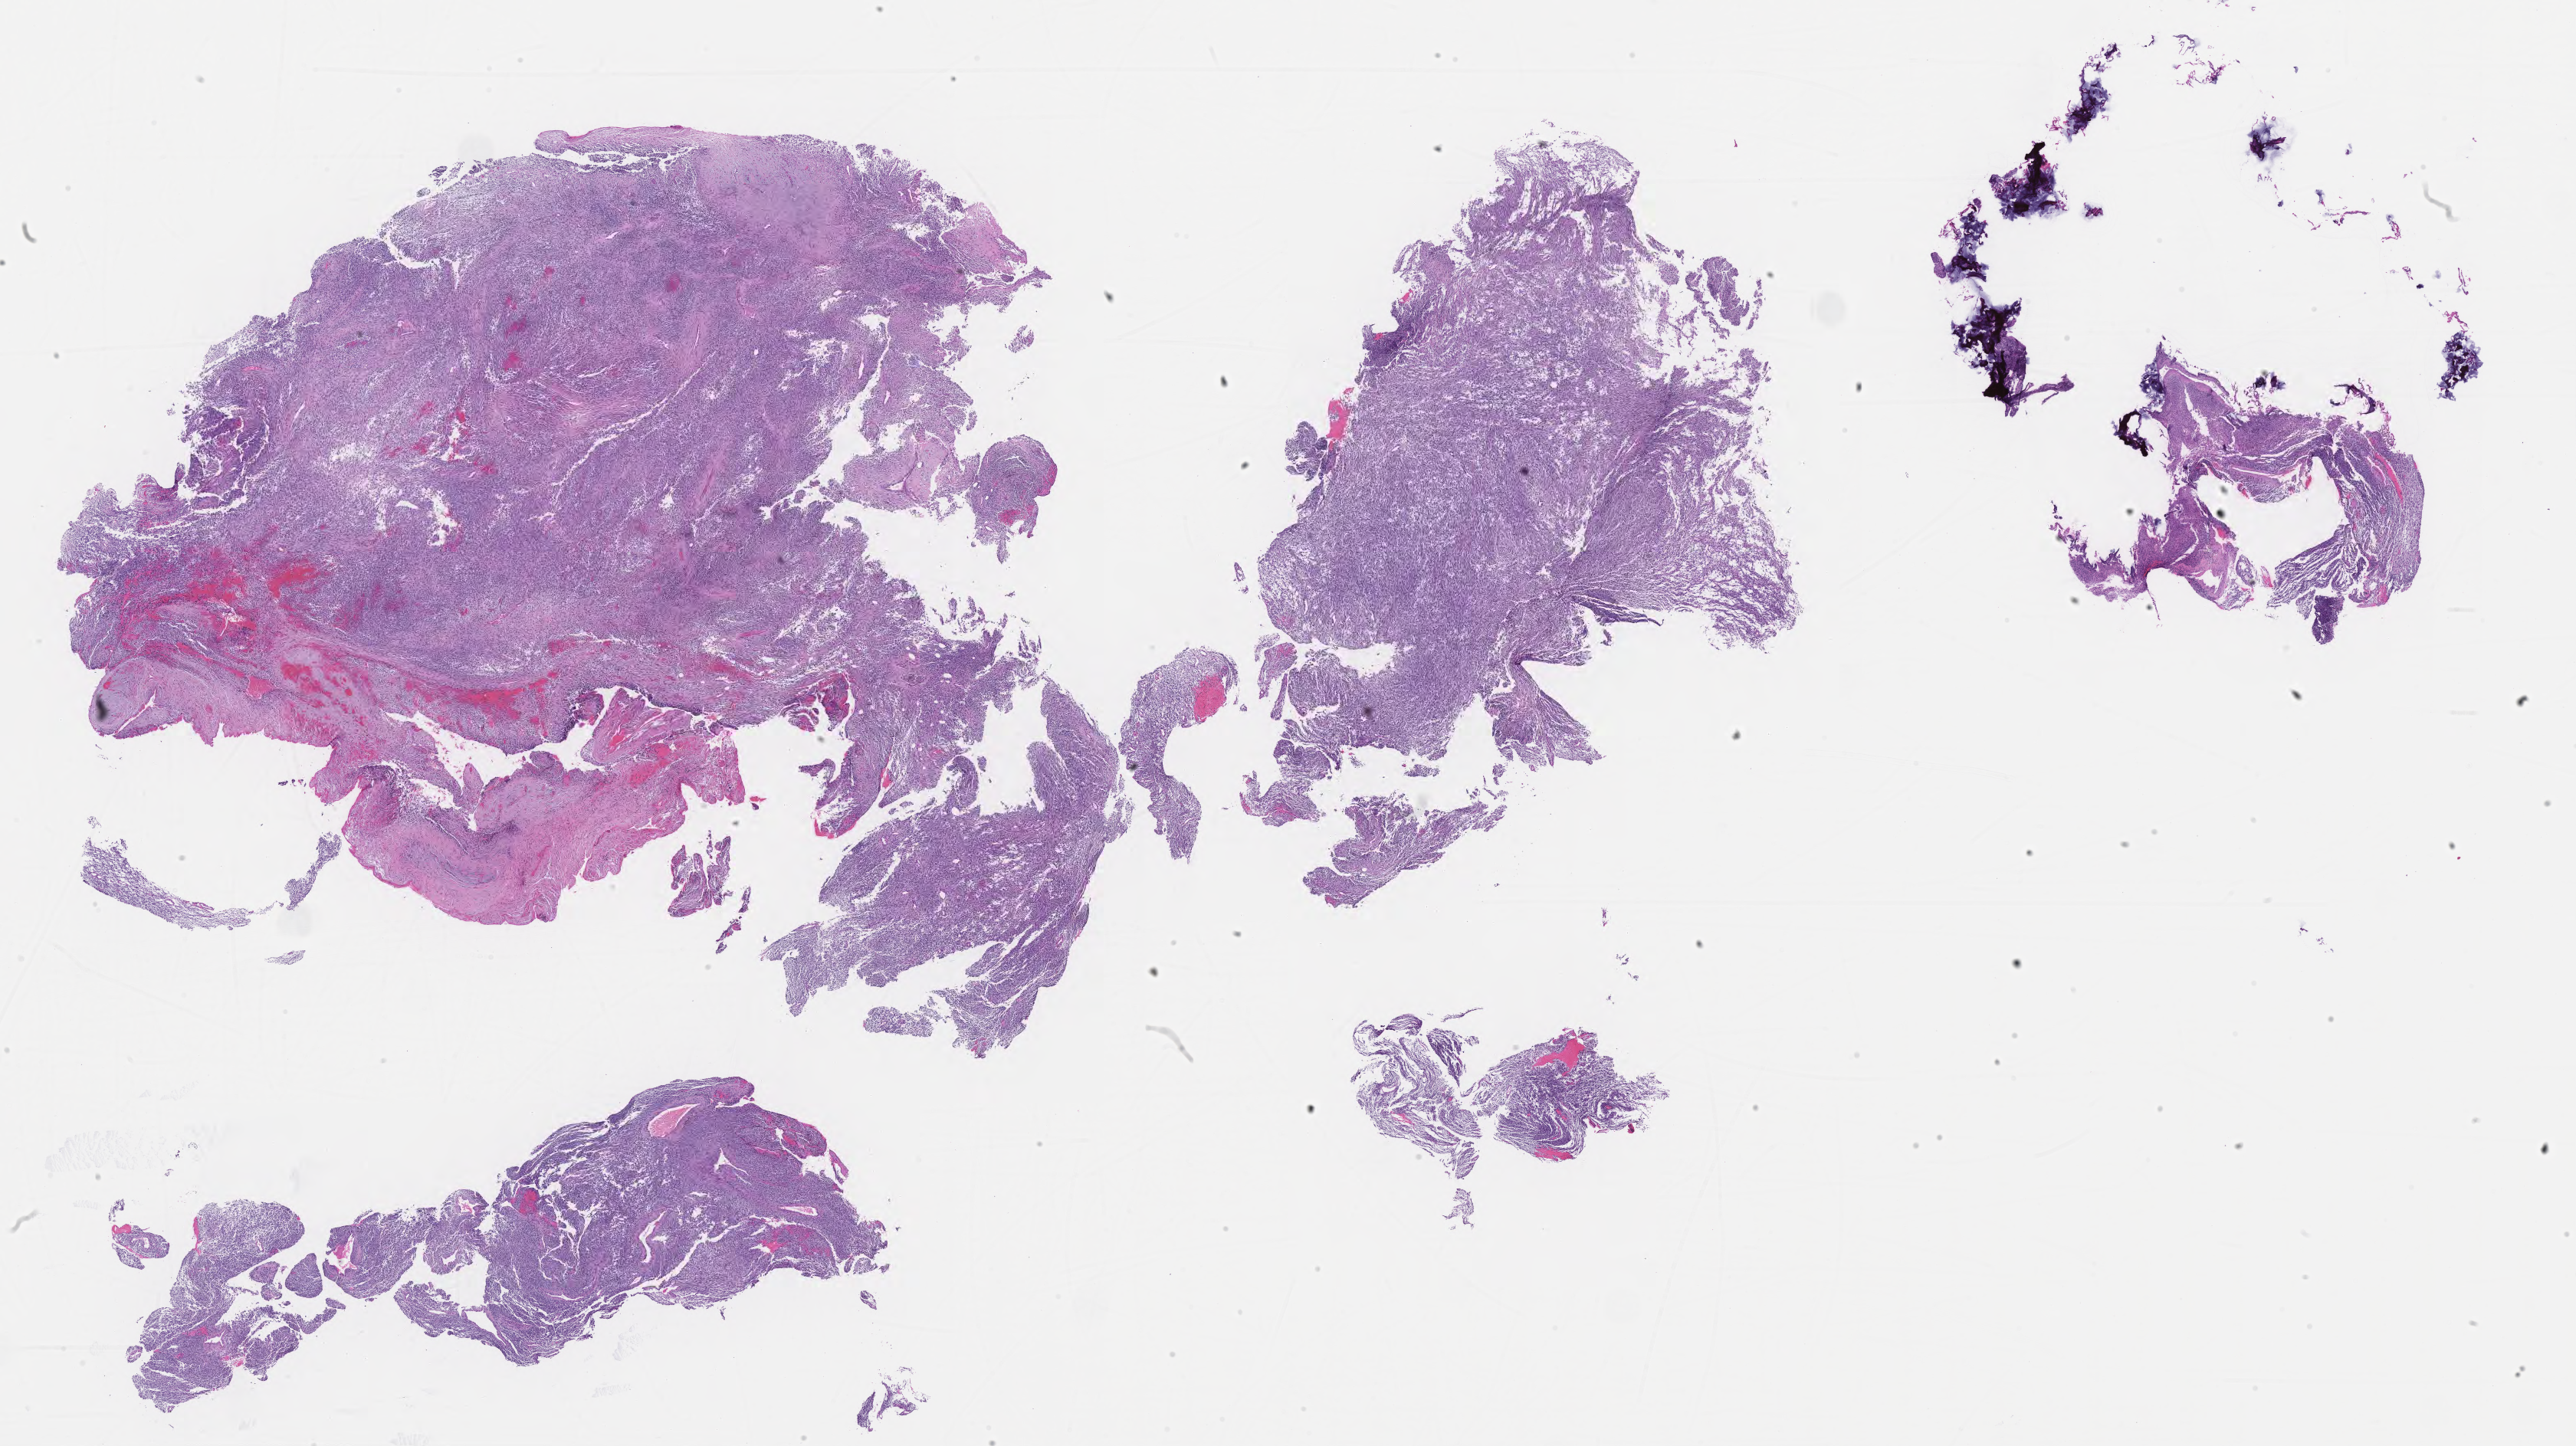
H&E whole-slide image of tumor tissue from the abdomen, a low-resolution overview of the entire scanned area, about 27.2 x 15.3 mm. FFPE section. Patient male; age 760 days.
Recorded diagnosis: Spindle cell rhabdomyosarcoma.